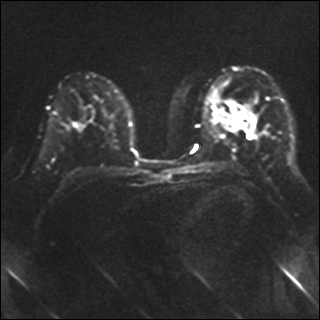
Breast MRI, one axial slice. Position 20 of 40 along the scan axis. Diffusion-weighted series; image 2 of 4 stored at this slice position (different b-values; order by instance number). 1.5 T. 4 mm slice thickness. 320 × 320 image matrix, field of view 320 × 320 mm. Female patient.
Structures marked on this image (expert manual segmentation):
- tumour on diffusion-weighted imaging: bounding box <230,104,251,129> (left, top, right, bottom; pixels)